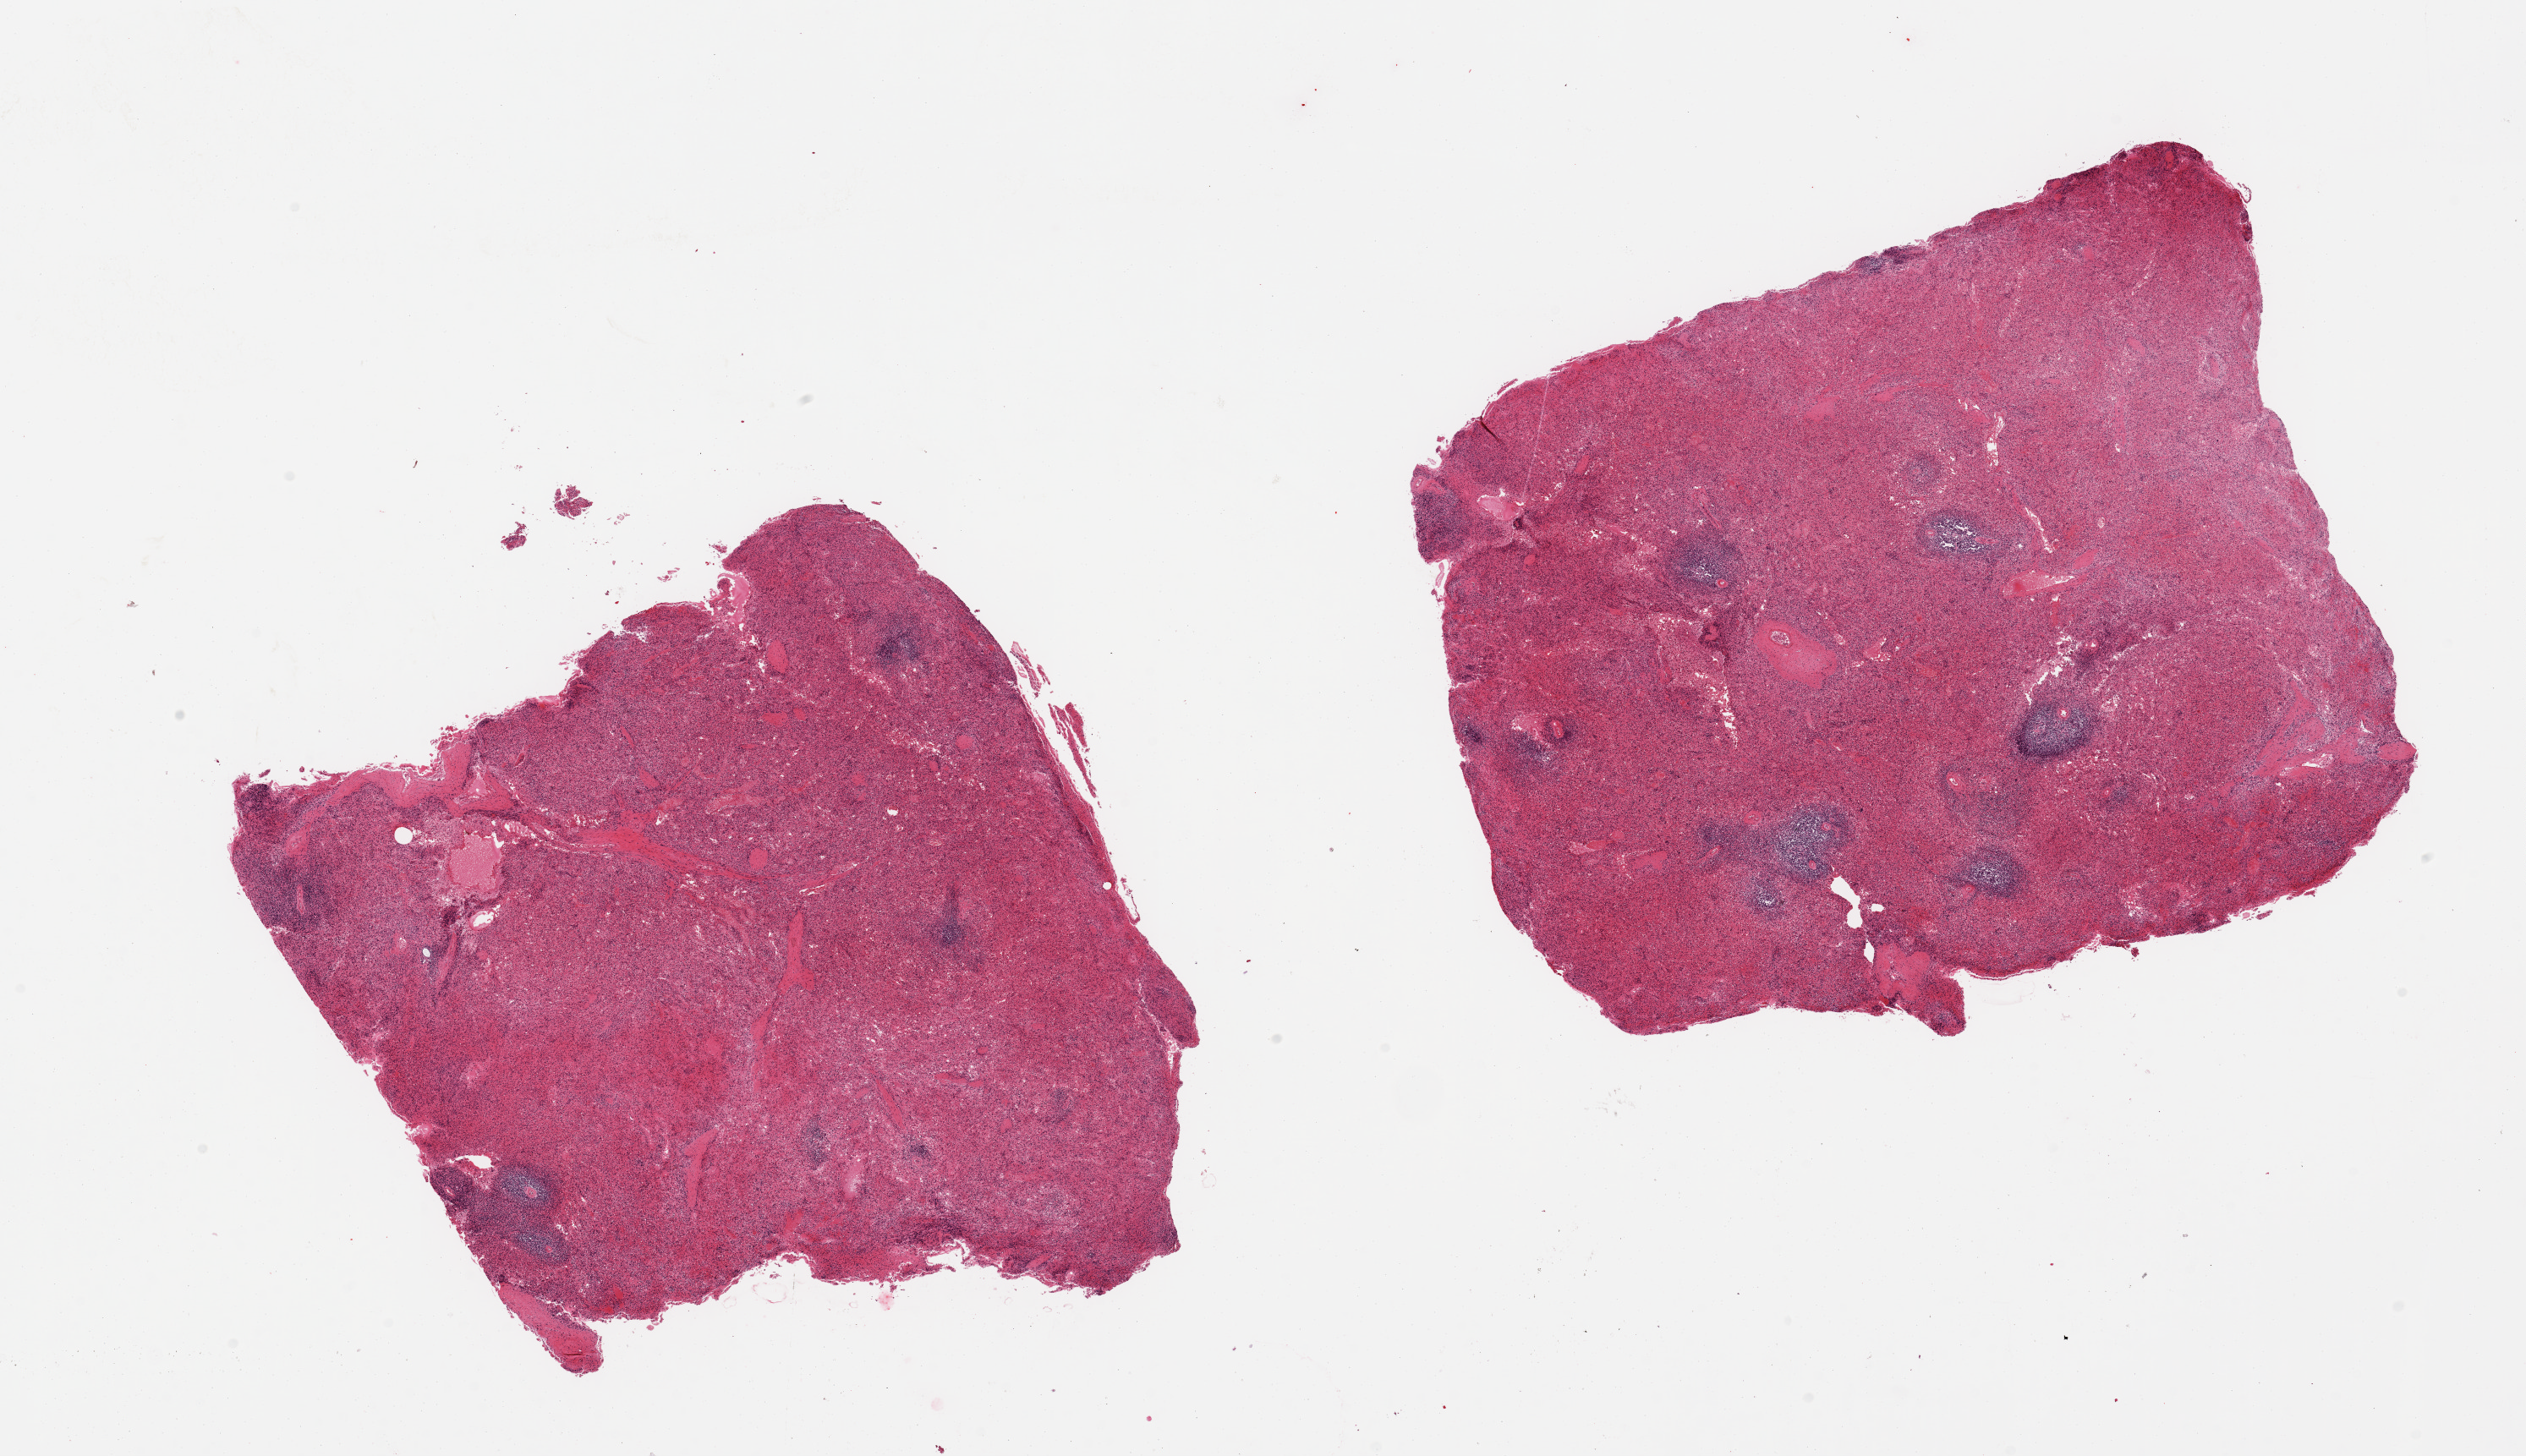
Whole-slide image, H&E stain — shown as a low-resolution overview of the whole scanned area (about 23.6 x 13.6 mm, acquisition: 20x scan), PAXgene-fixed paraffin-embedded (PFPE) section, sampled site (target tissue): spleen, tissue donor sample. Donor sex: female.
Review note (as recorded): 2 pieces; severely congested red pulp; intact white pulp.